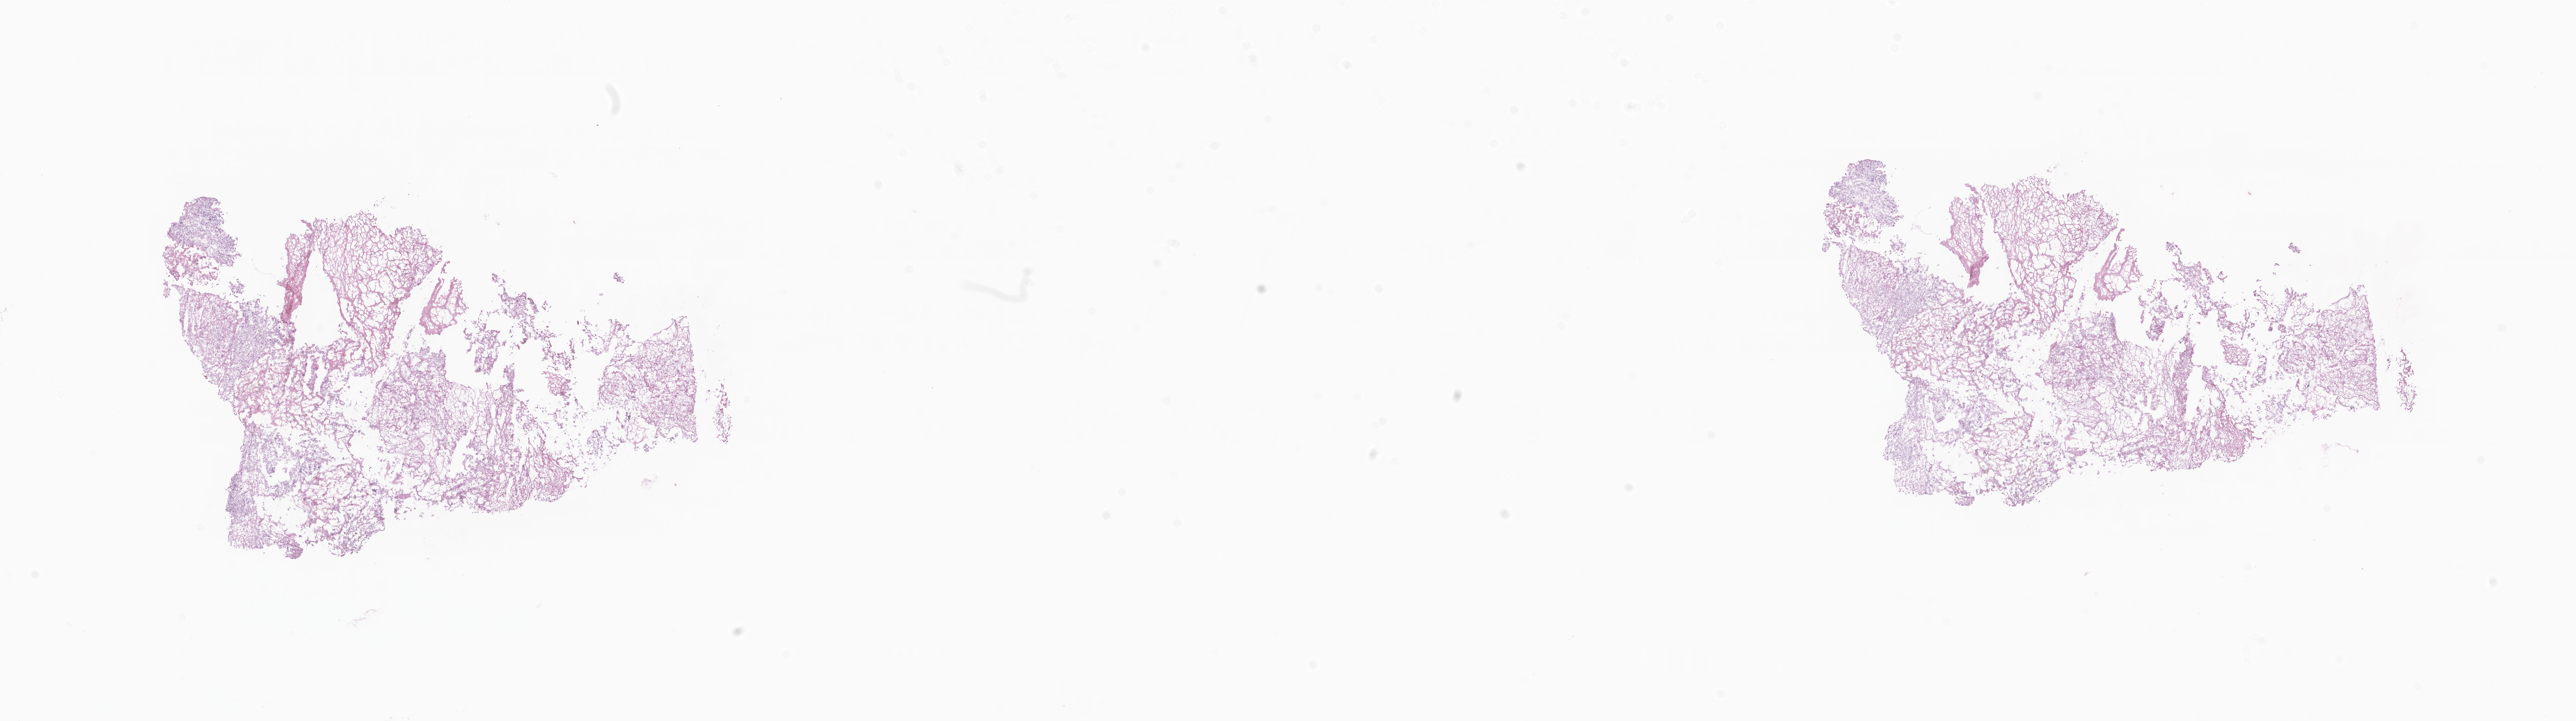
Digitized H&E-stained section, shown as a low-resolution overview of the whole scanned area (about 29.8 x 8.4 mm); frozen section (tissue freezing medium); specimen: metastatic tumor tissue. Female patient; age at initial diagnosis 67 years. Pathologist review of this section (percent, as recorded): tumor cells 30%, tumor nuclei 75%, stromal cells 57%, necrosis 13%, normal cells 0%. Inflammatory infiltration, as recorded: lymphocyte infiltration 12%, monocyte infiltration 2%, neutrophil infiltration 0%.
- section: top of the tissue portion
- patient diagnosis (primary): Giant cell sarcoma